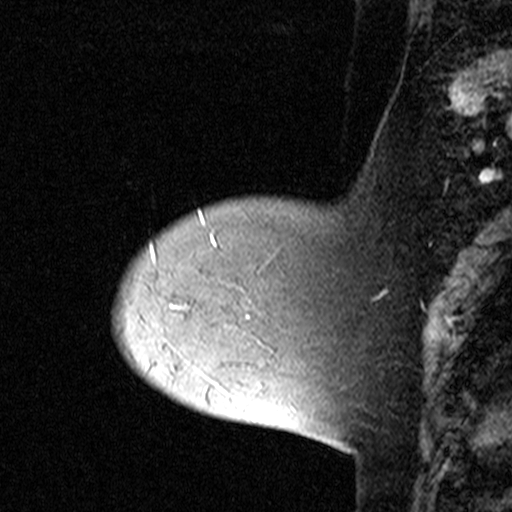
Breast MRI (dynamic contrast-enhanced), one sagittal slice. Slice 9 of 44 in the series (ordered by position). Dynamic contrast-enhanced study with each time point stored as its own series, time point 2 of 3 at this slice position (early post-contrast, ordered by acquisition time). 1.5 T. TE 4.5 ms, TR 11 ms. 3 mm slice thickness. 512 × 512 image matrix. Female patient, age 44 years. From the clinical record (not read from this slice): setting: breast cancer imaged before/during neoadjuvant chemotherapy; receptor status: triple-negative.
Structures marked on this image (semi-automatically segmented with operator editing):
- analysis volume of interest (the breast-tissue region the enhancement analysis was run in; not a lesion): bounding box (x1, y1, x2, y2) in pixels: (132, 212, 309, 331)
- tumour enhancement mask (voxels above the 90 % enhancement threshold inside the analysis volume of interest): (152, 221, 204, 255)